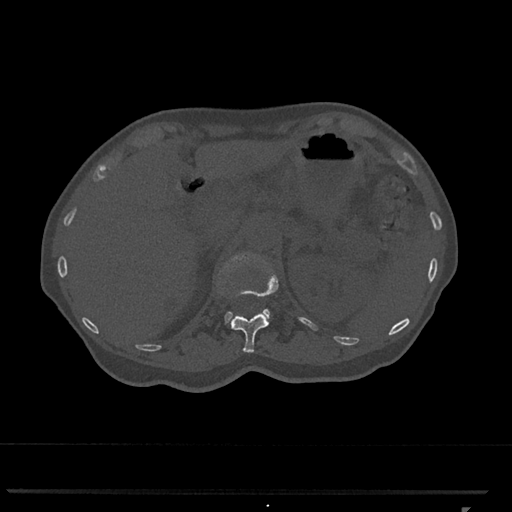
CT including the spine, one axial slice. Position 442 of 793 along the scan axis. 120 kVp. Bone window (W 1800 / L 400 HU). 512 × 512 image matrix, field of view 380 × 380 mm. Patient: female, 62 years. From the clinical record (not read from this slice): primary cancer: renal.
Structures marked on this image (semi-automatic segmentation, software-assisted and operator-edited):
- L1 vertebra: box from (x=225, y=253) to (x=270, y=324) px
- T12 vertebra: (x=227, y=255)–(x=279, y=353)